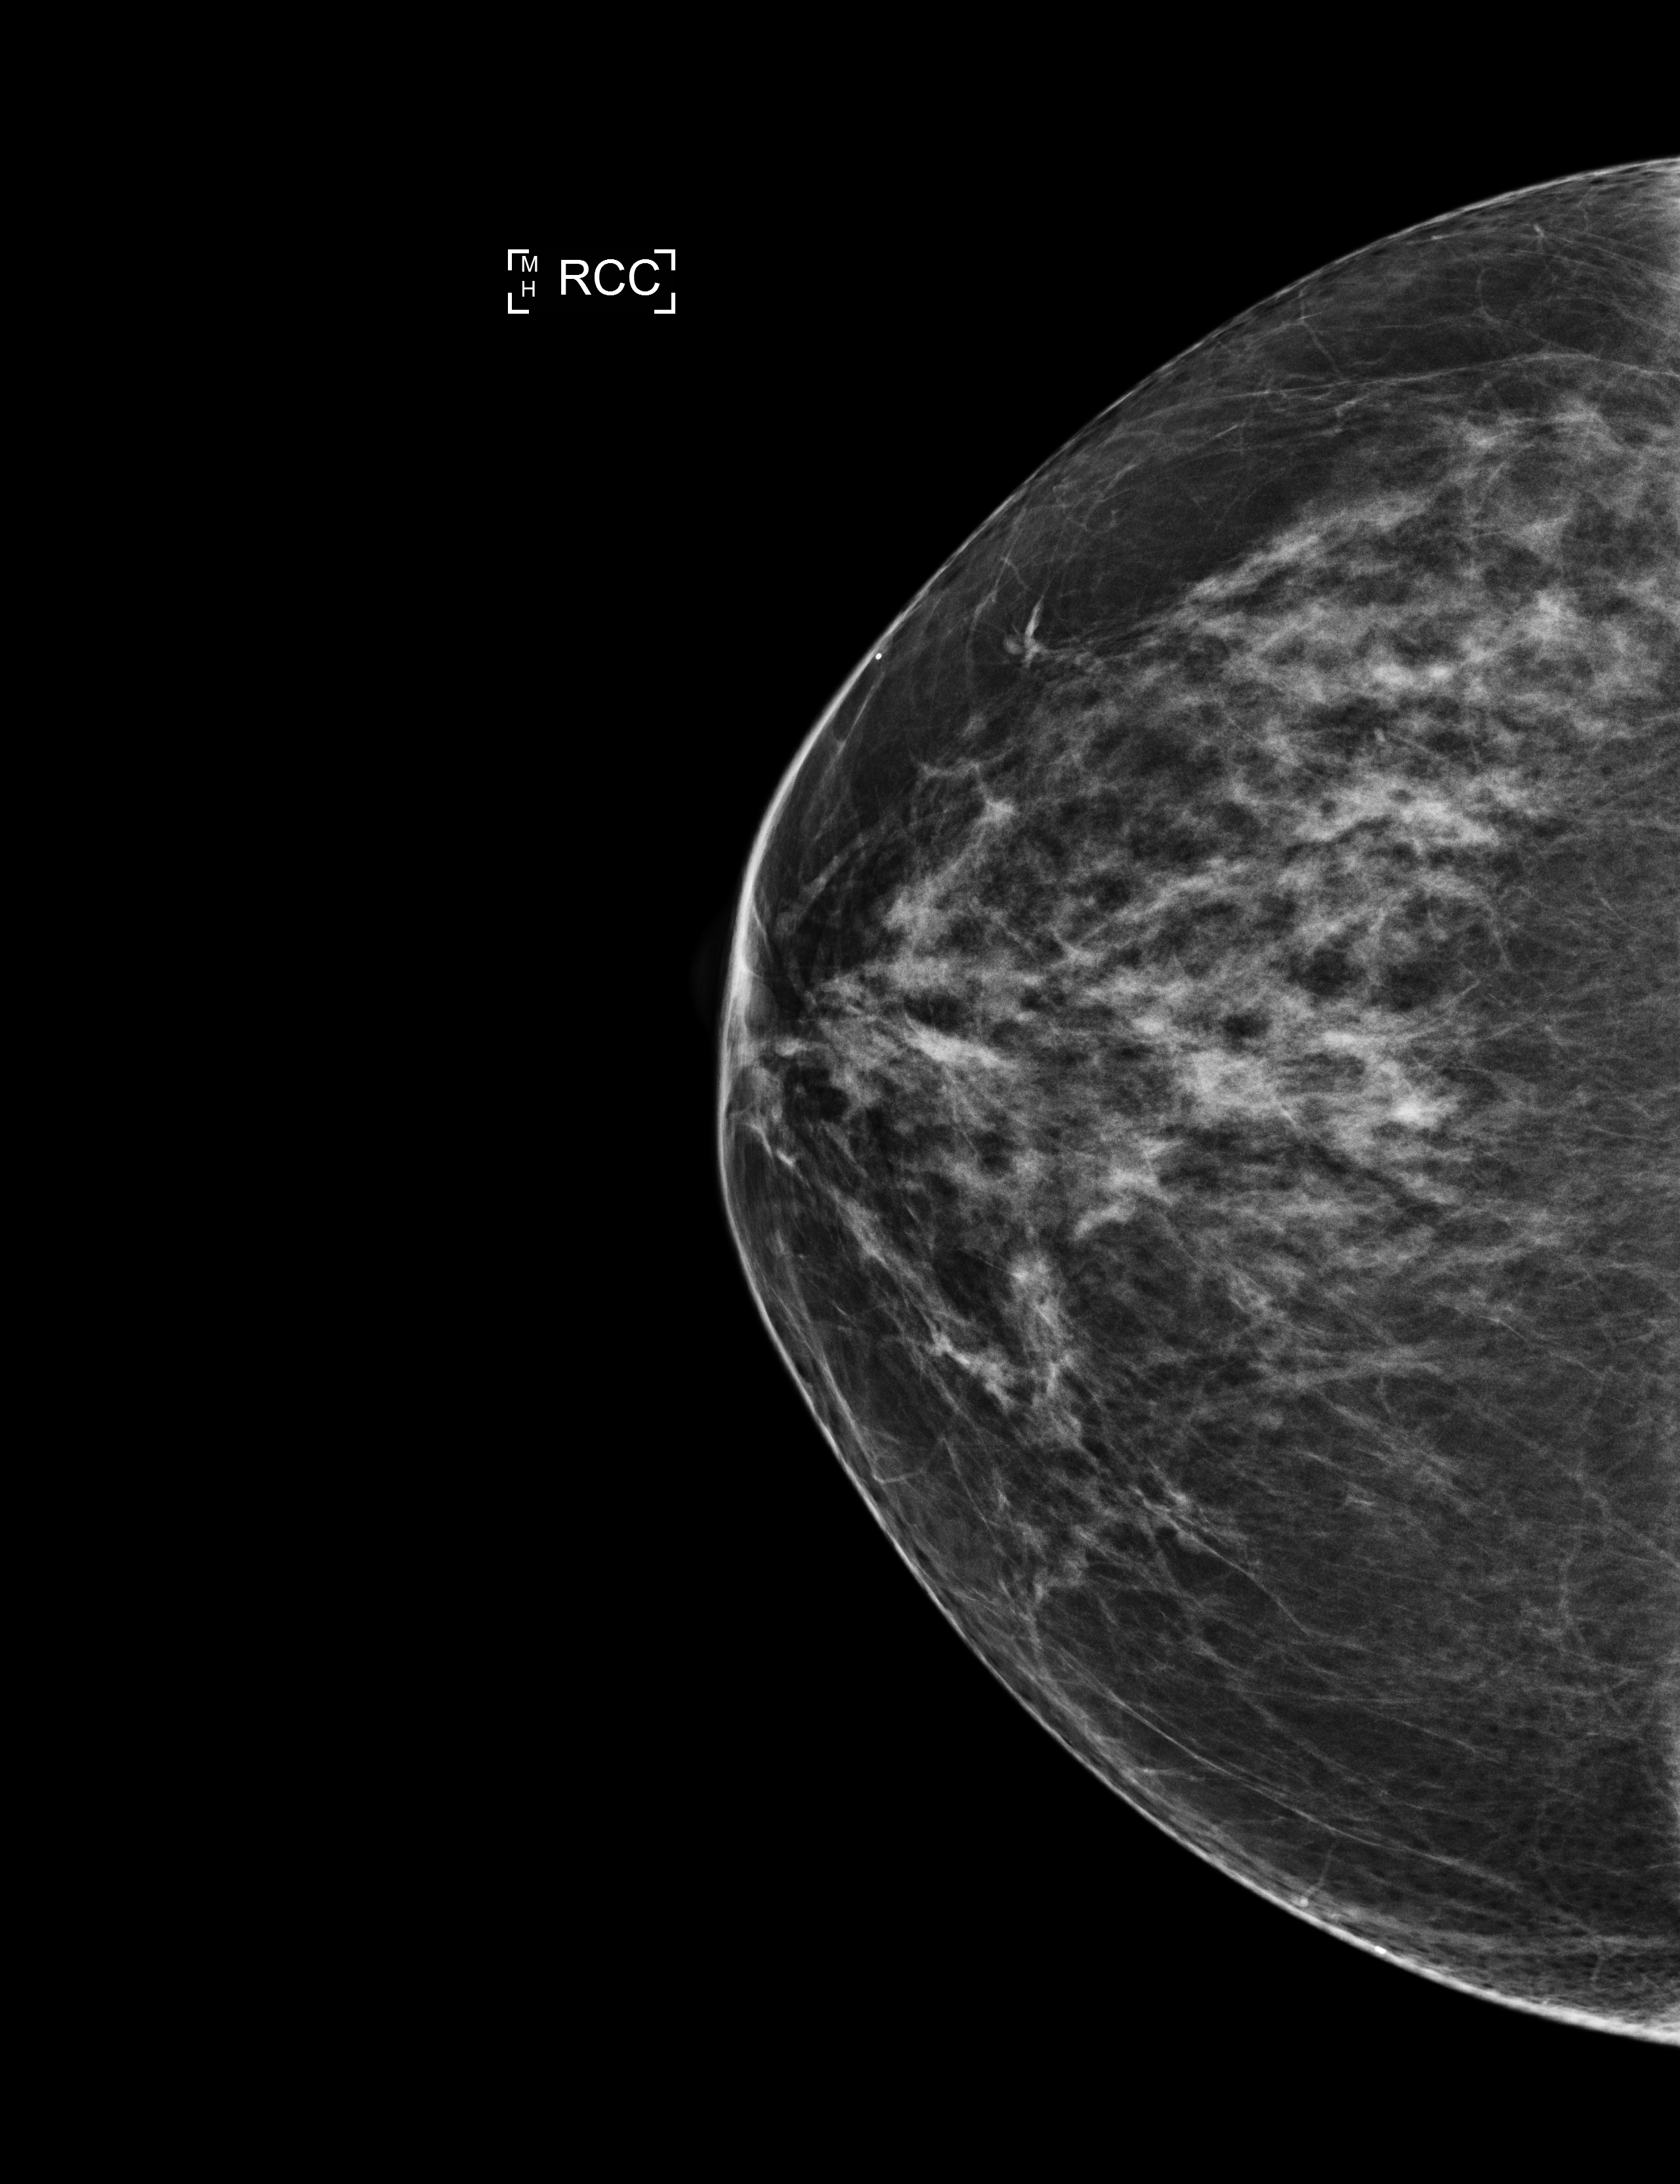
Screening examination. Female patient, age 71 years.
Image type: full-field digital mammogram. Breast: right. Projection: cranio-caudal projection.